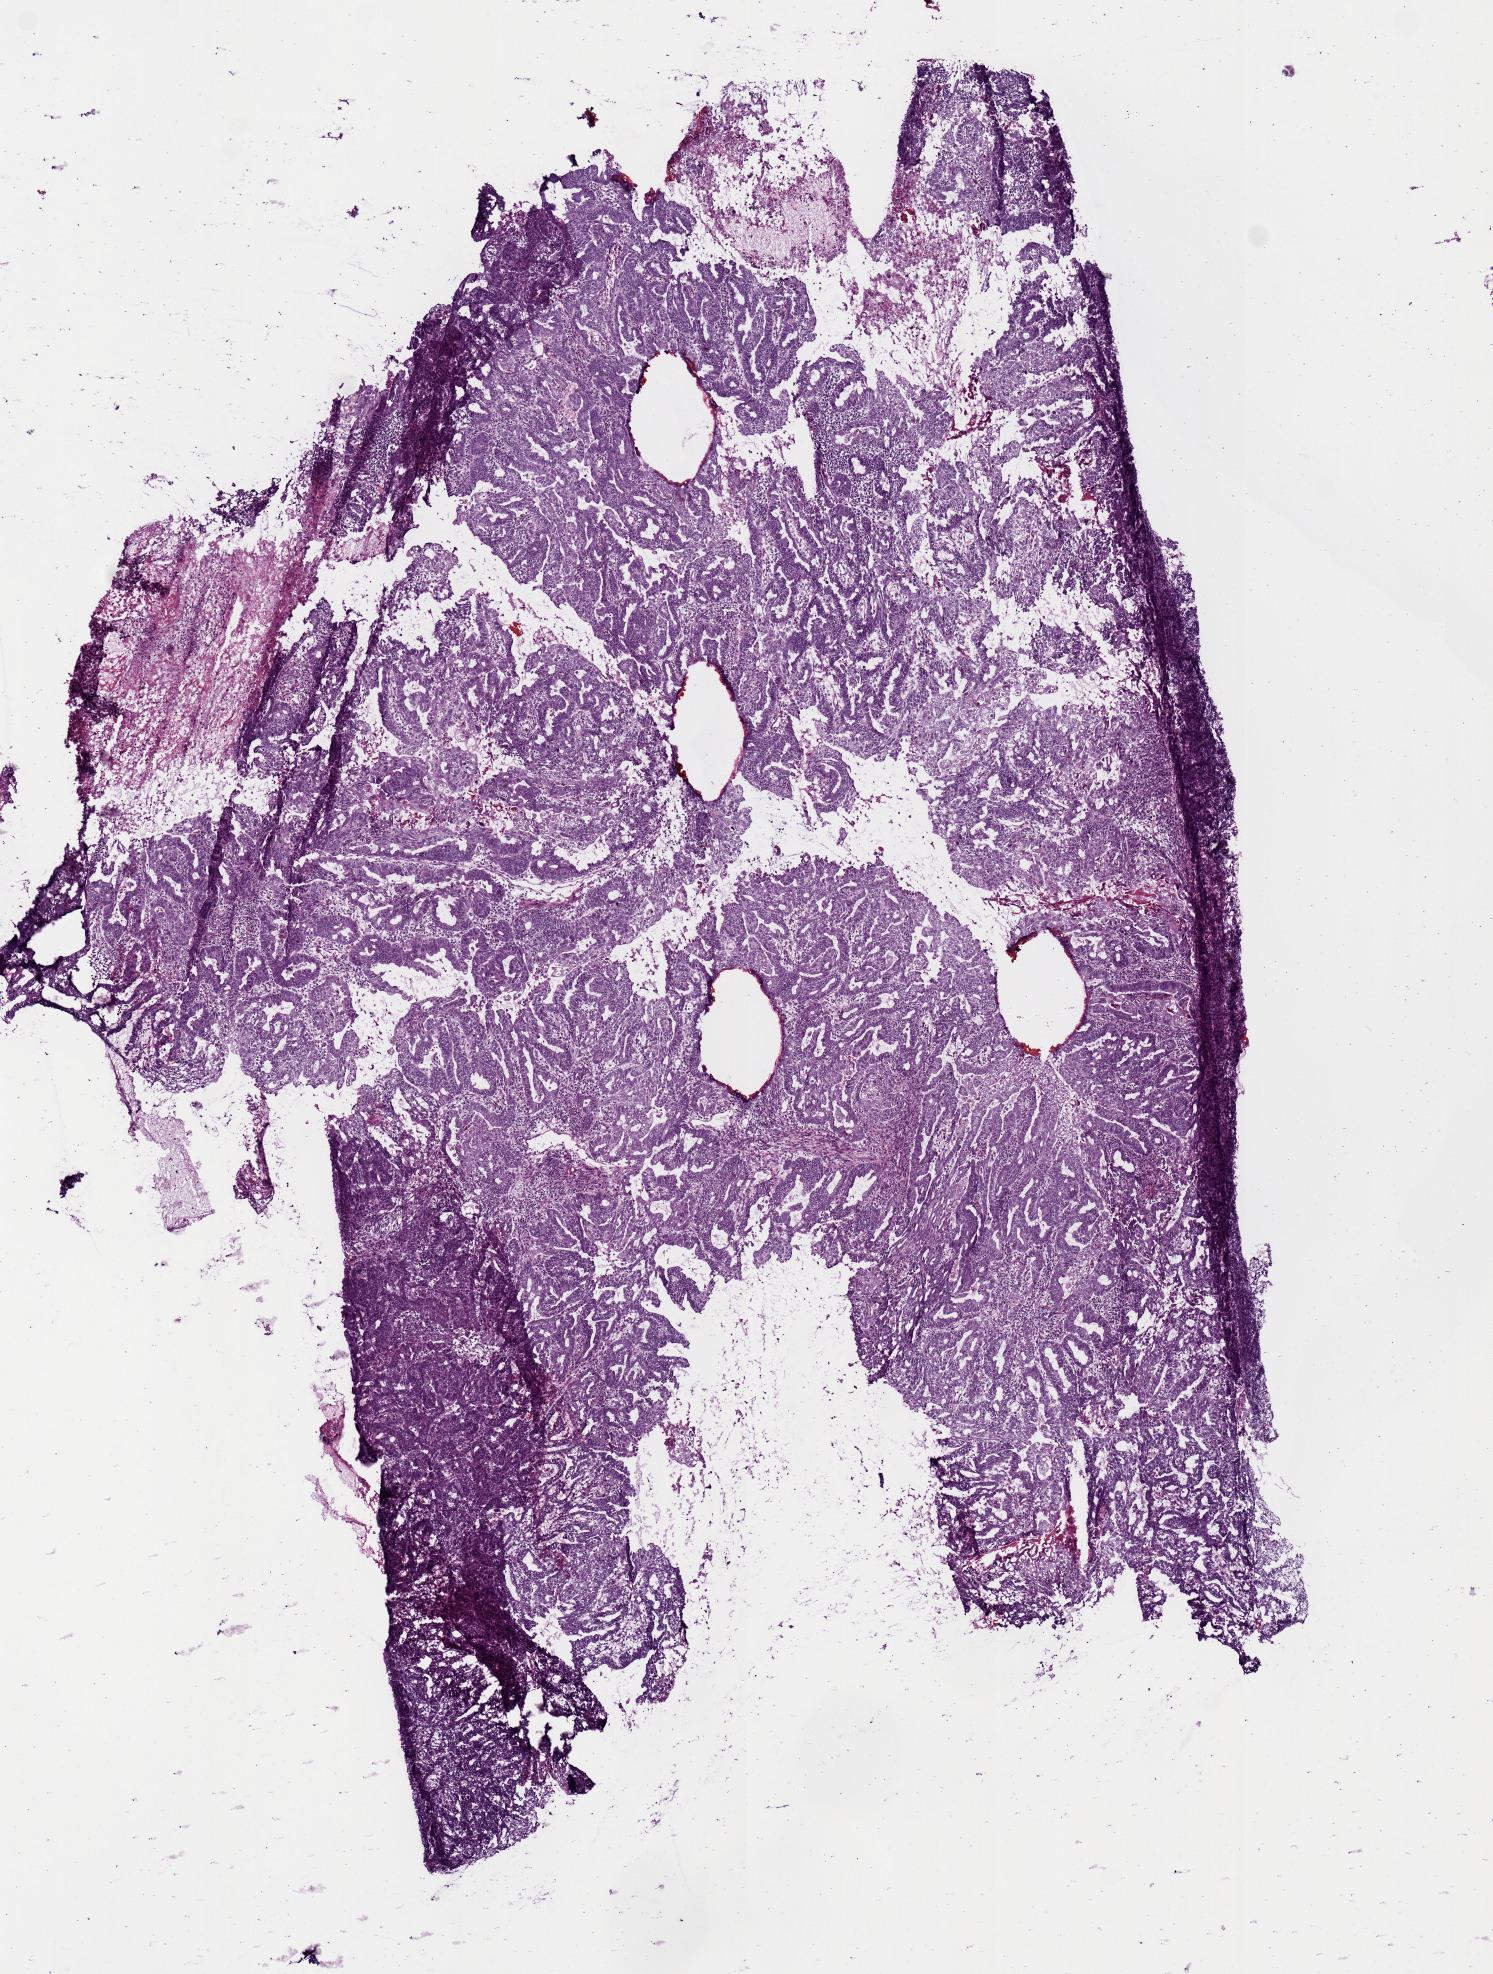
H&E whole-slide image — shown as a low-resolution overview of the whole scanned area (about 5.9 x 7.8 mm, from a 20x scan); frozen section from the bottom of the tissue portion; uterus, primary tumour sample. Female patient; age at initial diagnosis 46 years. Histologic grade: G3 (poorly differentiated). Pathologist review of this section (percent, as recorded): tumour cells 80%, tumour nuclei 65%, normal cells 0%, stromal cells 15%, necrosis 5%. Infiltration values recorded for this section: lymphocyte infiltration 0%, monocyte infiltration 0%, neutrophil infiltration 0%.
- FIGO stage: IA
- lymph nodes positive (case pathology): 0 of 12 examined
- pathologic diagnosis: Endometrioid adenocarcinoma, NOS (endometrium)